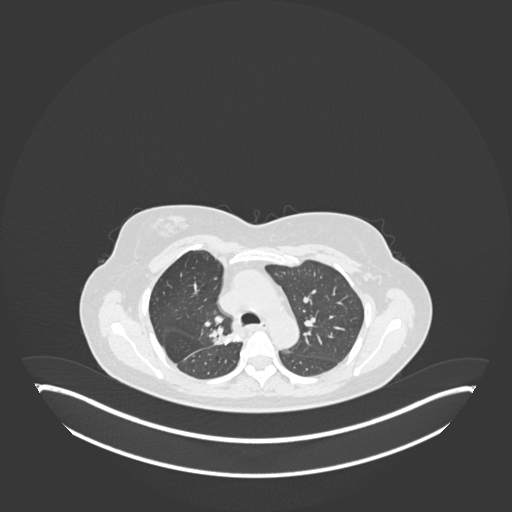
Chest CT, one axial slice; position 119 of 181 along the scan axis; reconstruction kernel B30f; 120 kVp; lung window (W 1500 / L -600 HU); 512 × 512 image matrix. Female patient, age 65 years. Case-level facts recorded for this patient, not image findings: clinical TNM (as recorded): T1b N0 M0; histopathological grade: G2.
Annotated regions visible in this slice (bounding box drawn by a radiologist):
- lung tumour (recorded histology: adenocarcinoma): bounding box <211,328,242,347> (left, top, right, bottom; pixels)